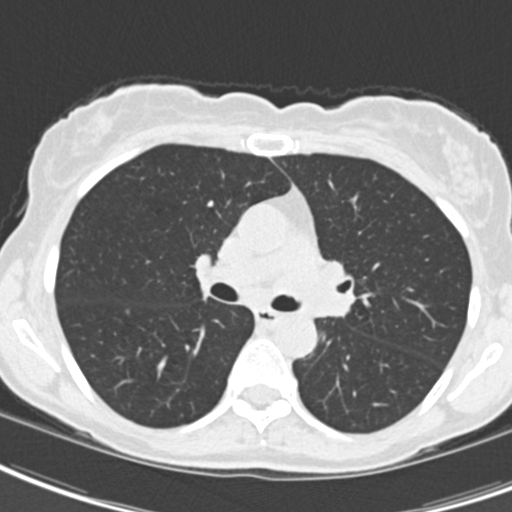
Low-dose screening chest CT, one axial slice. Position 123 of 189 along the scan axis. Reconstruction kernel B30f. Lung window (W 1500 / L -600 HU). 2 mm slice thickness. 512 × 512 image matrix.
Outlined on this slice (expert manual segmentation):
- lesion 2 (tumor, hilum of left lung): bounding box [x1, y1, x2, y2] px = [292, 262, 354, 316]